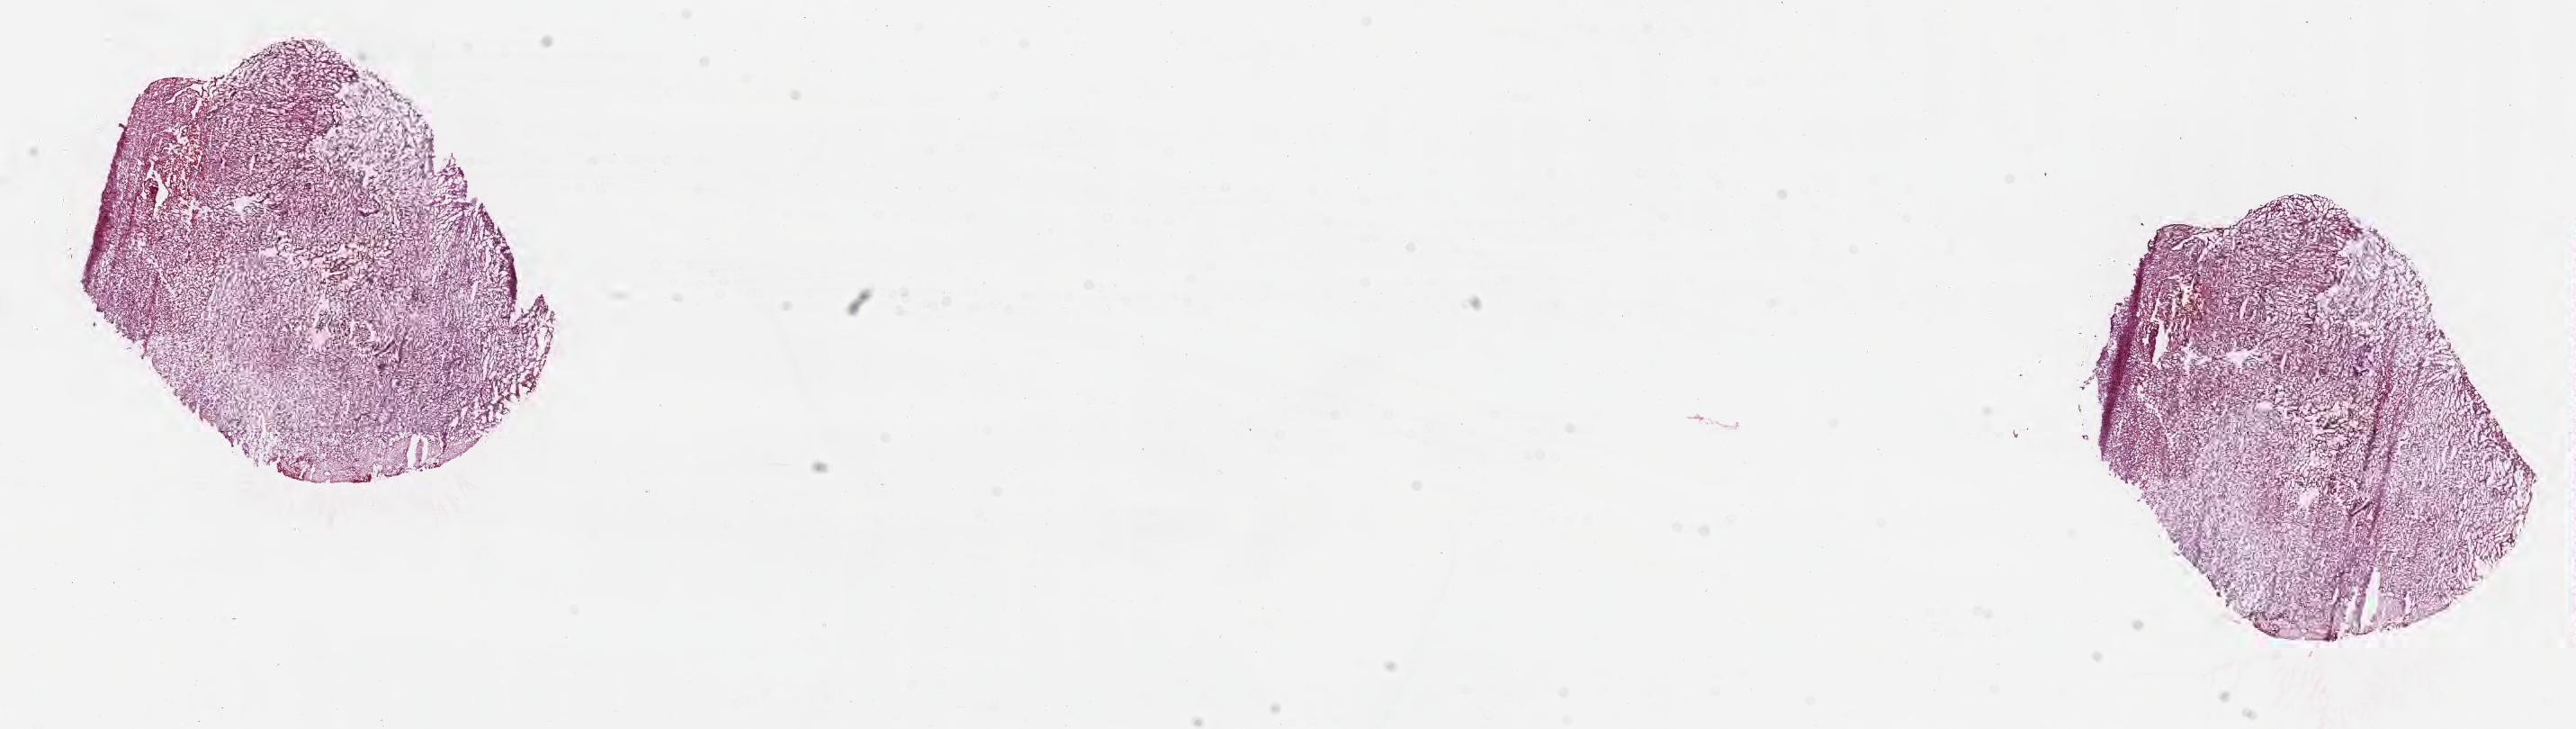
Digitized H&E-stained section — whole scanned area (about 23.2 x 6.6 mm) shown as a low-resolution overview, frozen section (tissue freezing medium), specimen: recurrent tumor, site: brain. Patient: male, age at initial diagnosis 63 years. Slide review estimates, as recorded: tumor cells 71%, tumor nuclei 91%.
Patient diagnosis: Glioblastoma, NOS.